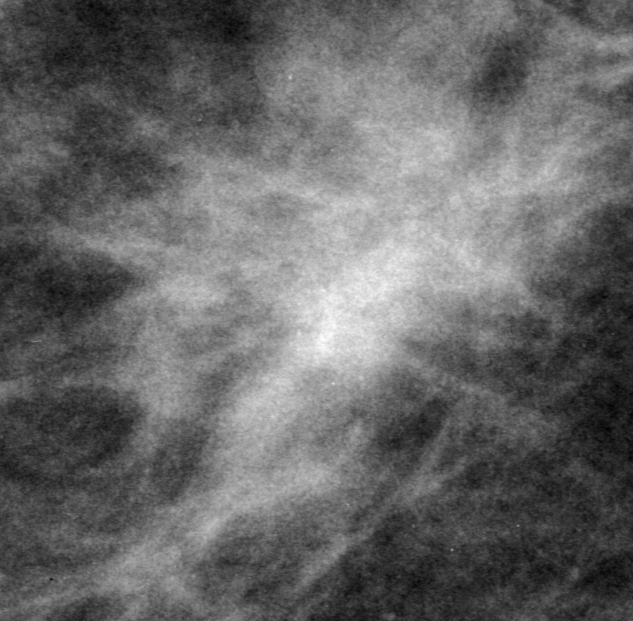
Region of interest cut from a scanned film mammogram (one marked finding), right breast, CC view.
Mass, shape architectural distortion; BI-RADS assessment category 0 (incomplete: needs additional imaging); pathology result (as recorded, not read from the image): malignant.